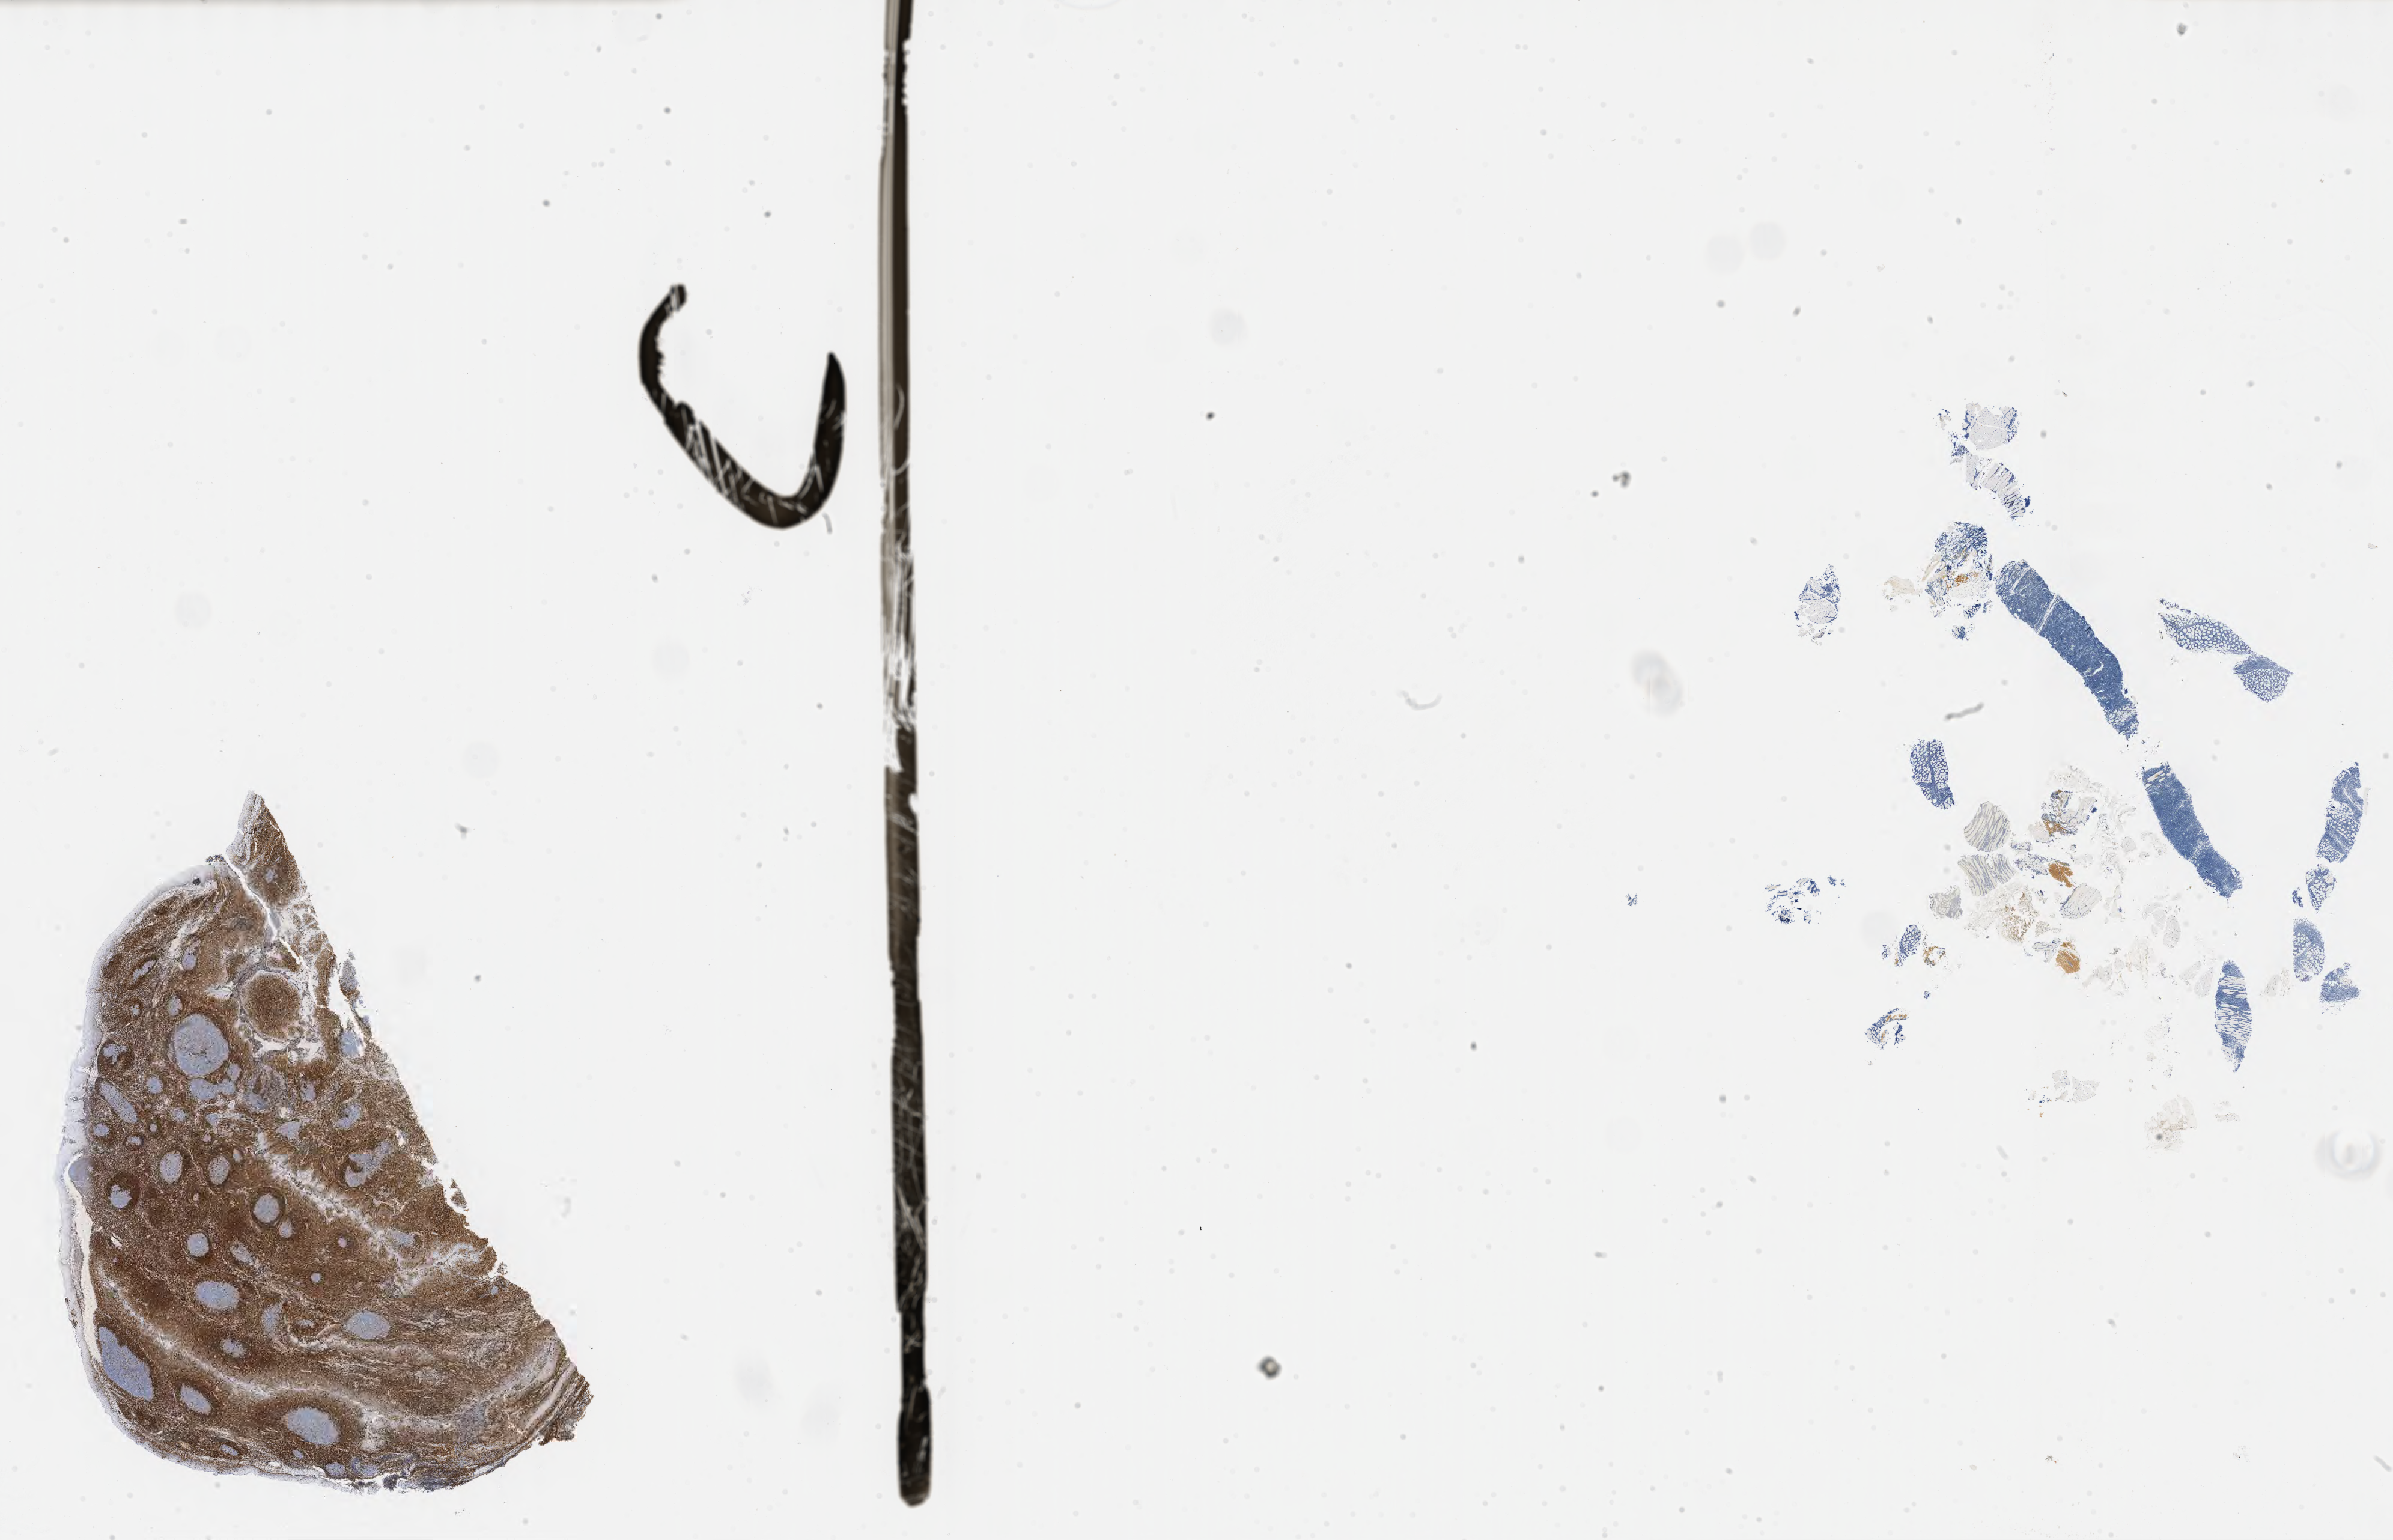
IHC for BCL2, whole-slide image, low-resolution overview of the scanned area, about 32.2 x 20.7 mm; tumor tissue; anatomic site: retroperitoneum. Patient female; 53 years old.
- histologic diagnosis: Burkitt lymphoma, NOS